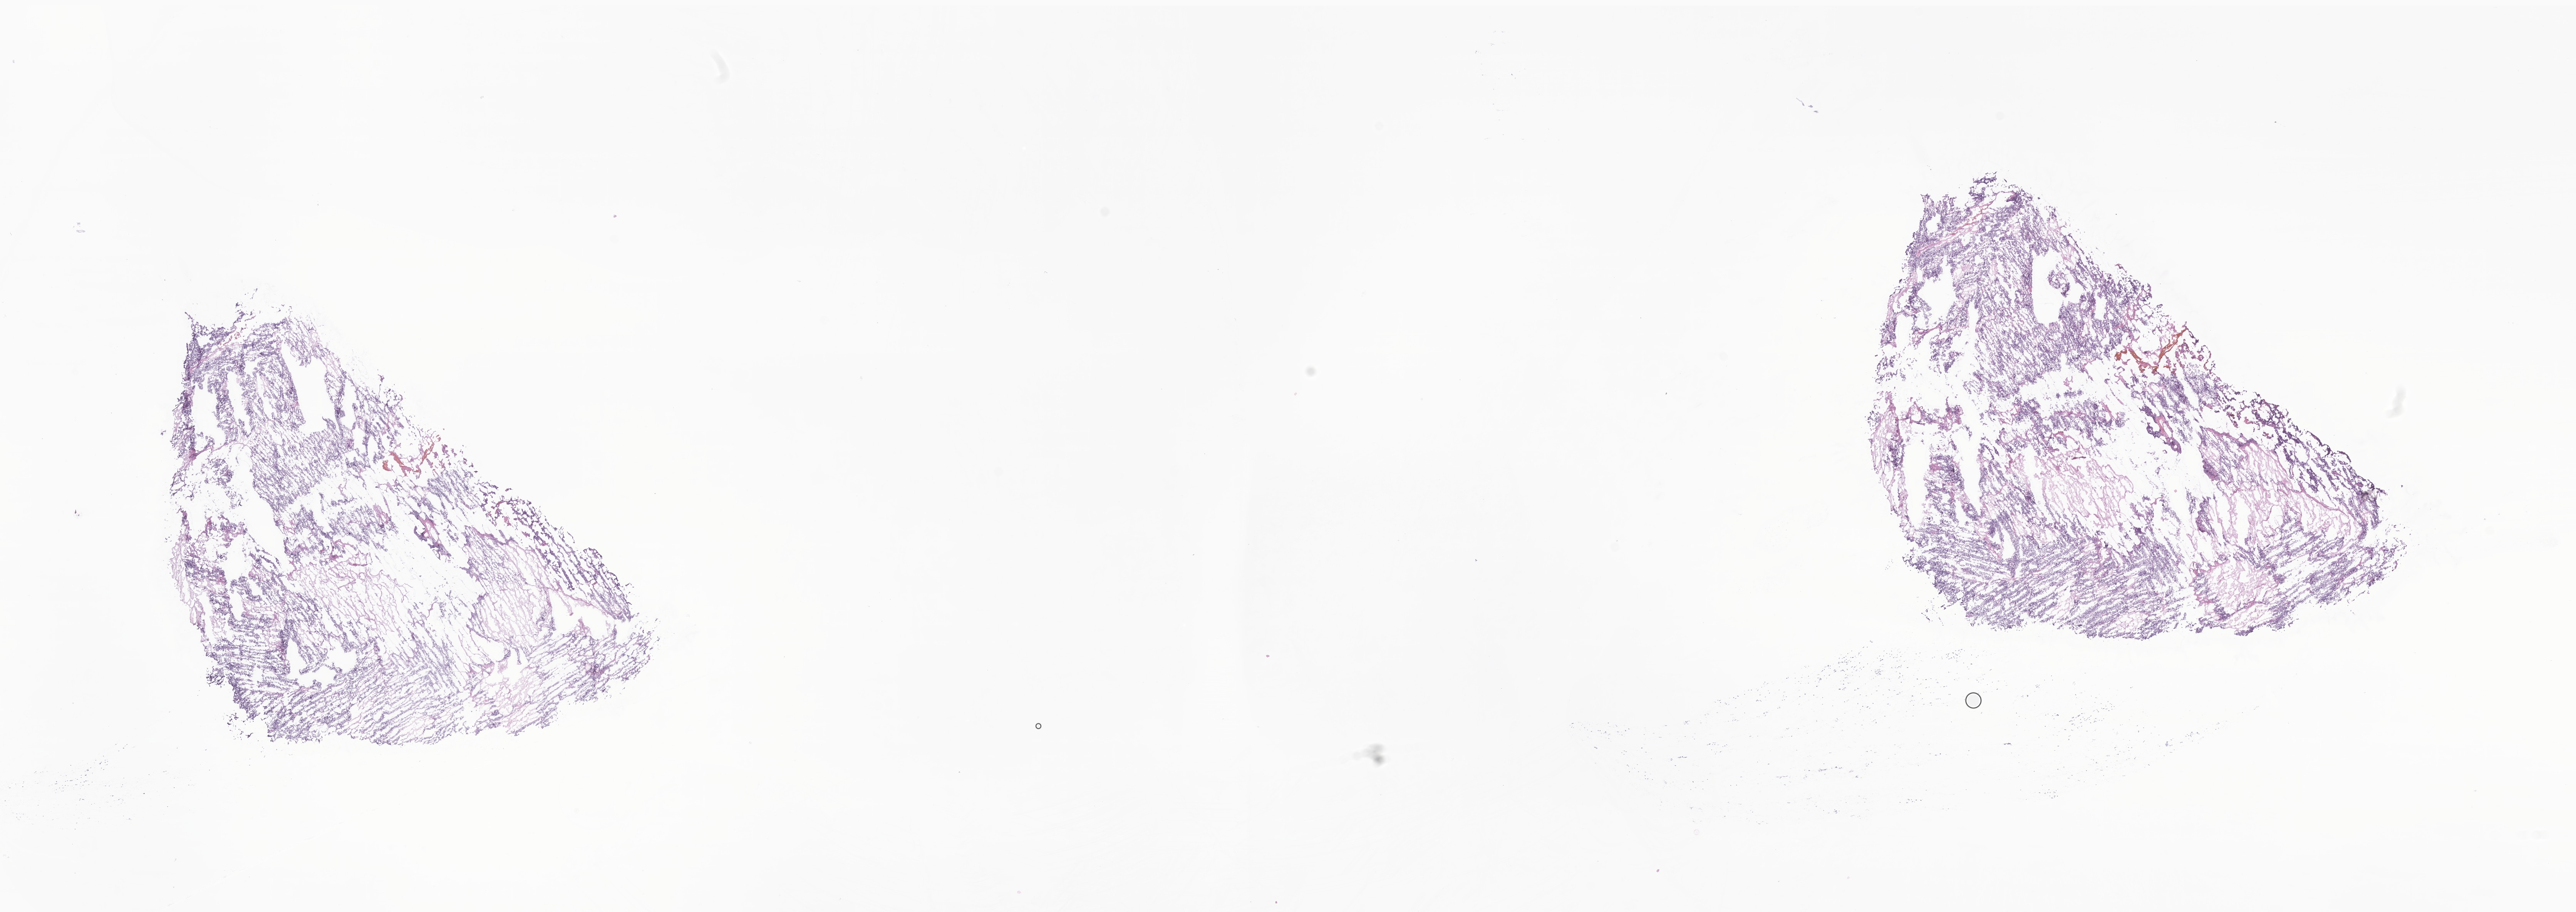
Digitized H&E-stained section of tumor tissue from the brain, low-resolution overview of the scanned area, about 28.2 x 10.0 mm. Frozen section. Patient male; age 47 months (3 years 11 months).
Diagnosis (ICD-O-3 morphology term): Neoplasm, benign.